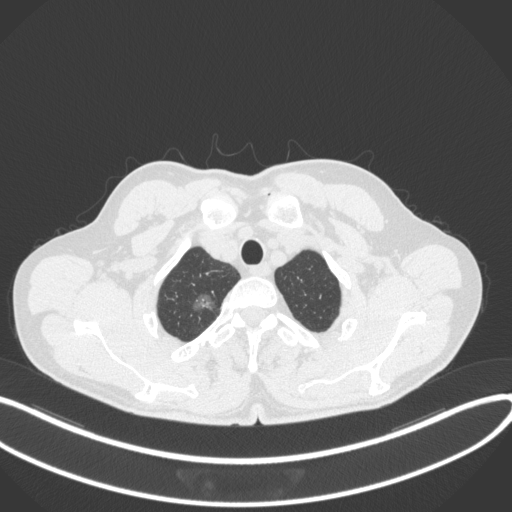
Chest CT, one axial slice. Slice 346 of 407 in the series (ordered by position). Reconstruction kernel B31f. 120 kVp. Lung window (W 1500 / L -600 HU). 1 mm slice thickness. 512 × 512 image matrix. Male patient, age 58 years. Case-level facts recorded for this patient, not image findings: clinical TNM (as recorded): T1c N0 M0; histopathological grade: G1-2.
Outlined on this slice (rectangle marked by the reading radiologist):
- lung tumour (recorded histology: adenocarcinoma): bounding box (x1, y1, x2, y2) in pixels: (189, 289, 219, 319)